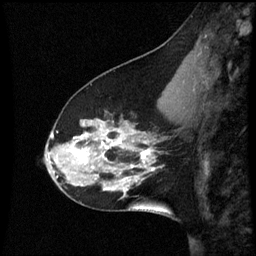
Breast MRI (dynamic contrast-enhanced), one sagittal slice. Position 20 of 60 along the scan axis. Dynamic contrast-enhanced series, image 2 of 3 at this slice position (ordered by acquisition). 1.5 T. TE 4.2 ms, TR 8.9 ms. 2 mm slice thickness. 256 × 256 image matrix. Female patient, age 45 years. From the clinical record (not read from this slice): setting: breast cancer imaged before/during neoadjuvant chemotherapy; receptor status: HR-positive, HER2-negative.
Annotated regions visible in this slice (semi-automatic segmentation, software-assisted and operator-edited):
- analysis volume of interest (the breast-tissue region the enhancement analysis was run in; not a lesion): bounding box [x1, y1, x2, y2] px = [46, 94, 171, 205]
- tumour enhancement mask (voxels above the 70 % enhancement threshold inside the analysis volume of interest): [52, 130, 155, 191]